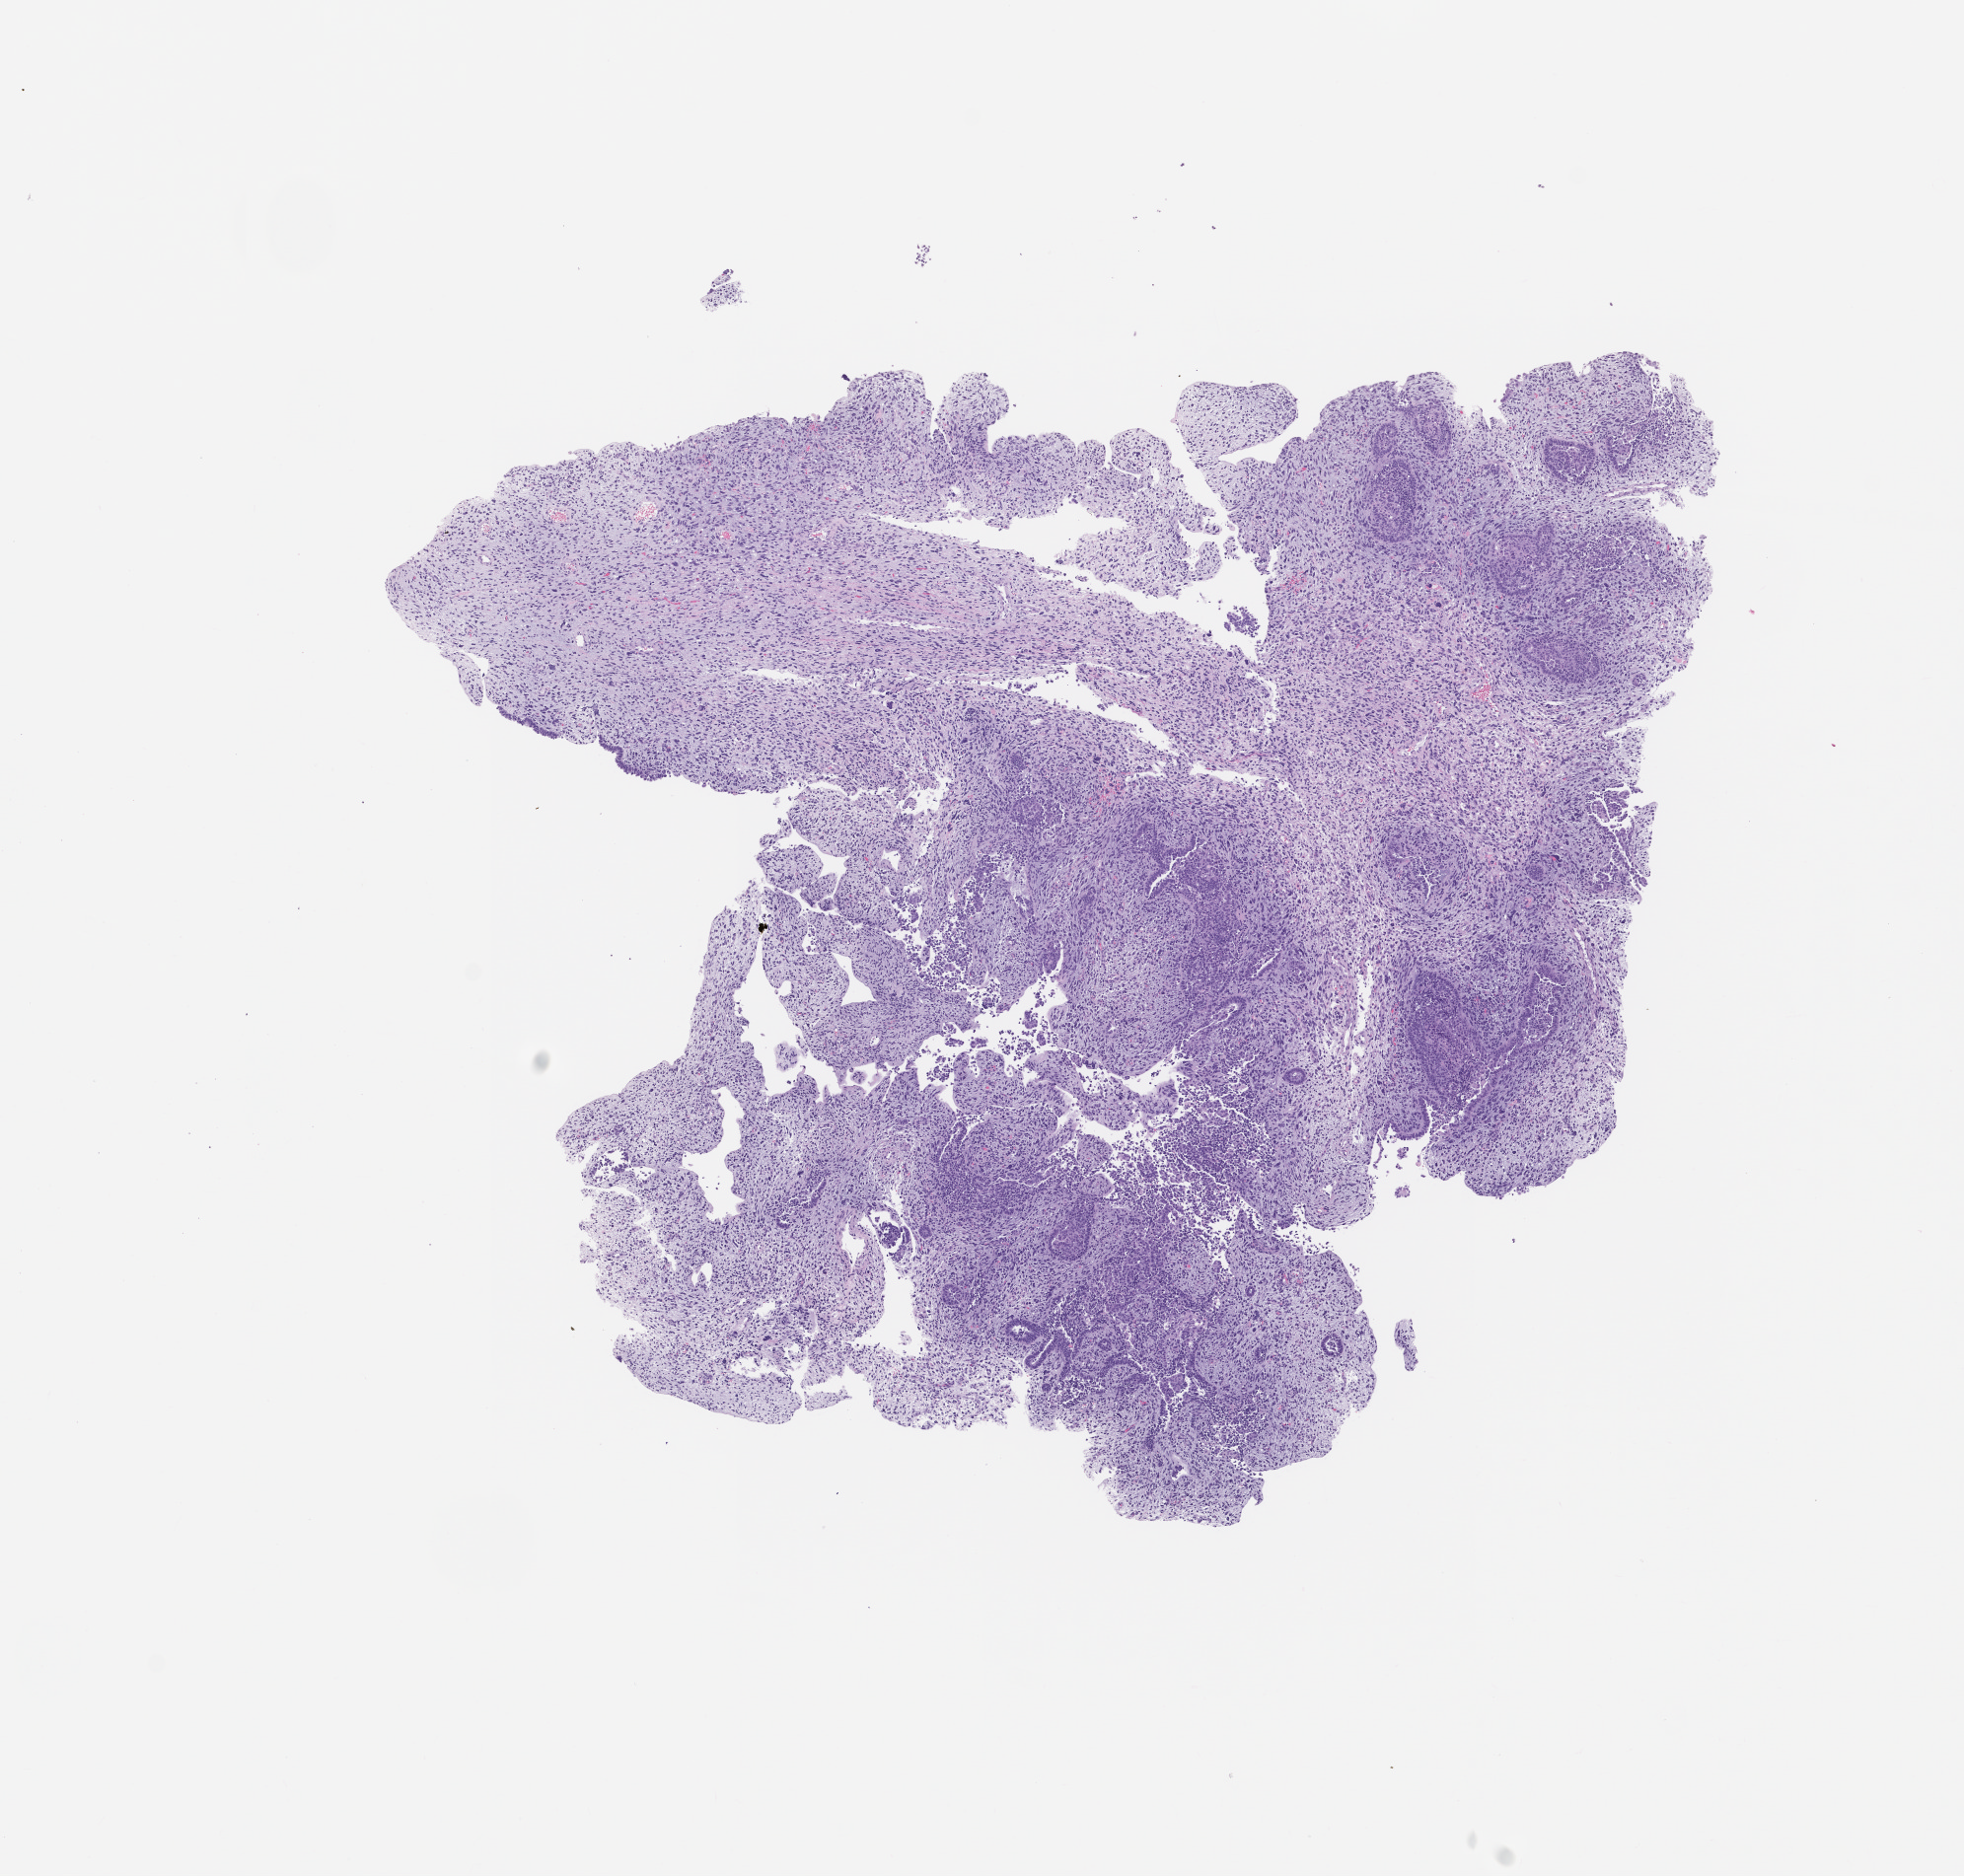
H&E whole-slide image of the patient's (originator) tumor tissue, a low-resolution overview of the entire scanned area, about 8.0 x 7.6 mm; formalin-fixed, paraffin-embedded (FFPE) tissue; originating tumor site category: uterus. Patient female; aged 57.
Diagnosis: Carcinosarcoma.